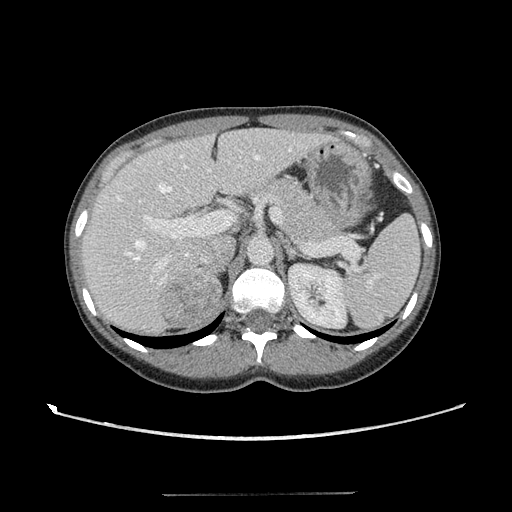
Contrast-enhanced abdominal CT, one axial slice; position 76 of 117 along the scan axis; reconstruction kernel STANDARD; intravenous contrast given; soft-tissue window (W 400 / L 40 HU); 2.5 mm slice thickness; 512 × 512 image matrix. Patient: female, 35 years. Case-level facts recorded for this patient, not image findings: diagnosis: adrenocortical carcinoma; tumour side: right adrenal; tumour size at pathology: 3 cm; Ki-67 index: 21 %; stage (as recorded): 3.
Annotated regions visible in this slice (semi-automatic segmentation, software-assisted and operator-edited):
- mass: bounding box (x1, y1, x2, y2) in pixels: (162, 269, 219, 324)